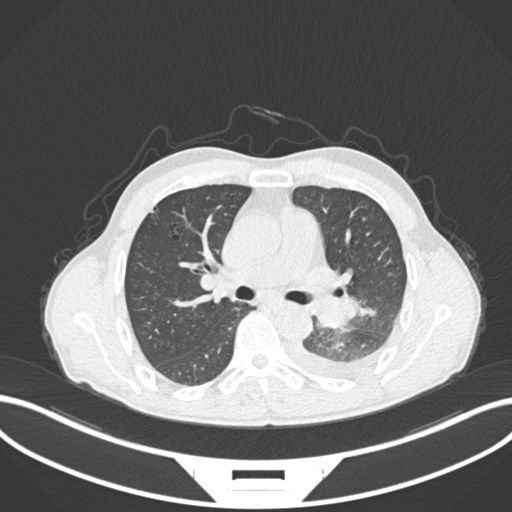
Chest CT, one axial slice. Slice 151 of 222 in the series (ordered by position). Reconstruction kernel B30f. 120 kVp. Lung window (W 1500 / L -600 HU). 1 mm slice thickness. 512 × 512 image matrix, field of view 400 × 400 mm. Patient: male, 47 years. From the clinical record (not read from this slice): clinical TNM (as recorded): T3 N1 M1c; histopathological grade: G3.
Annotated regions visible in this slice (bounding box drawn by a radiologist):
- lung tumour (recorded histology: small cell carcinoma): bounding box [x1, y1, x2, y2] px = [308, 291, 360, 331]